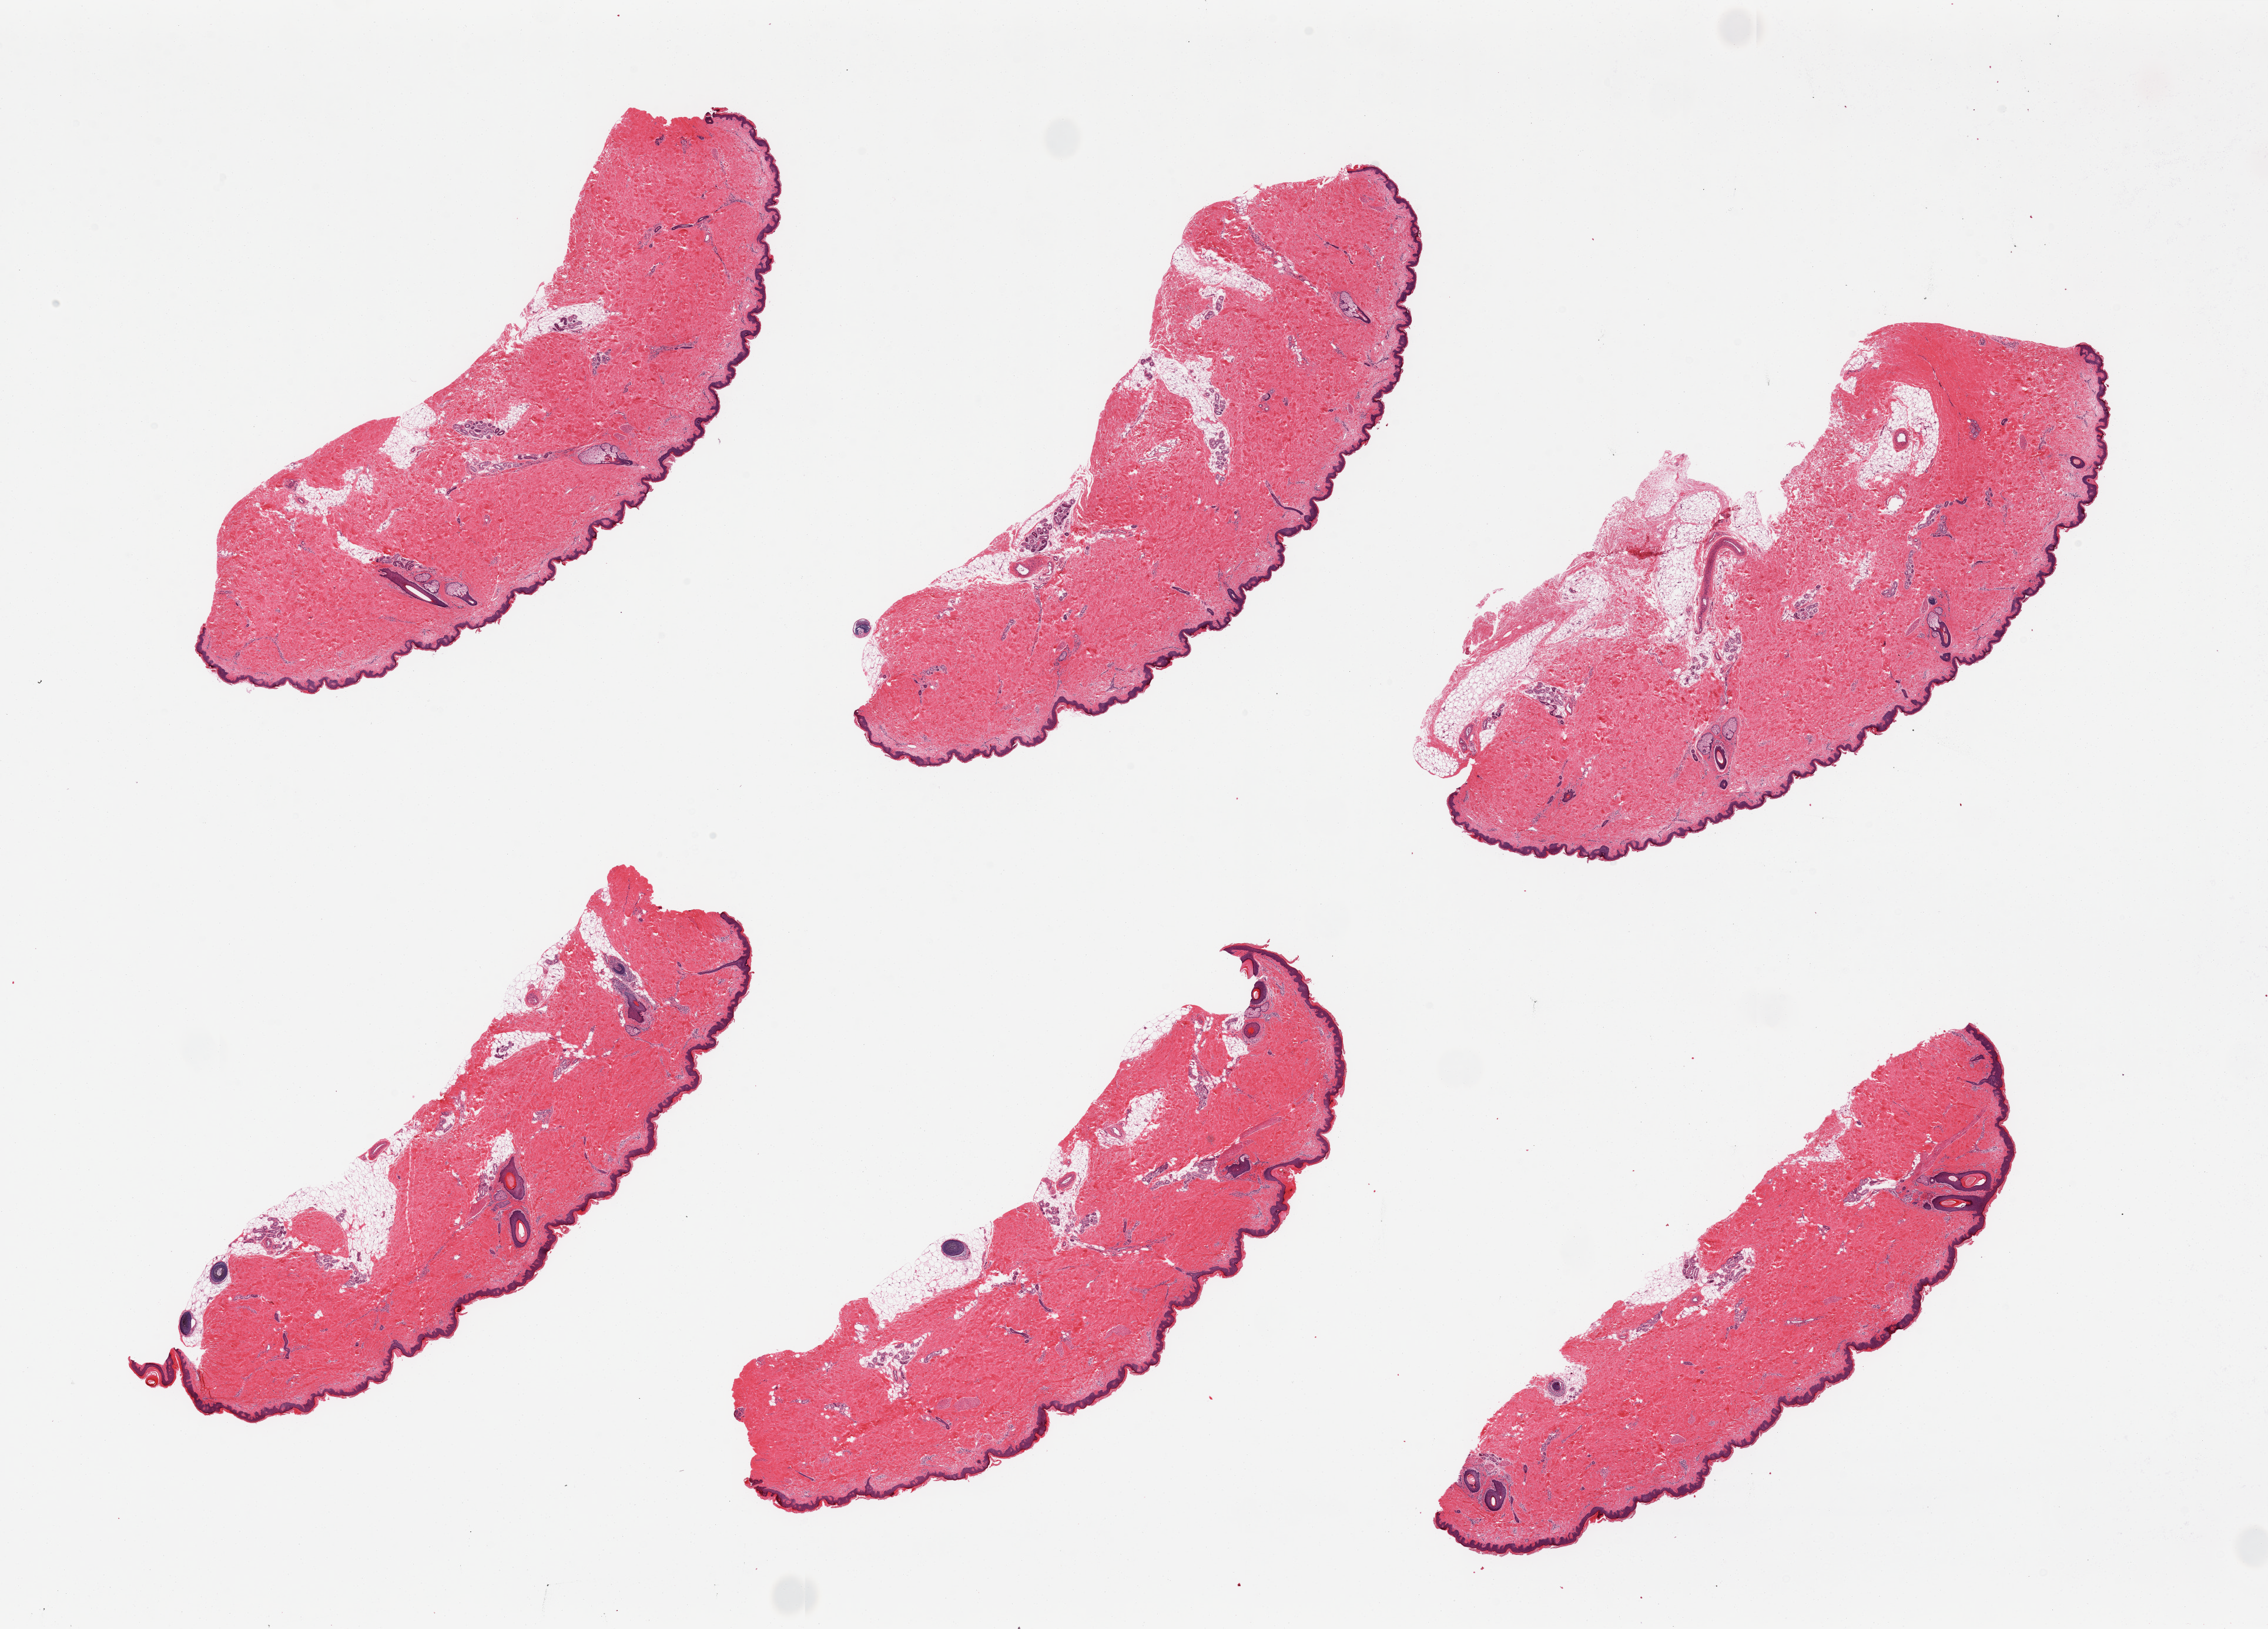
Whole-slide image, H&E stain — low-resolution overview of the scanned area, about 30.5 x 21.9 mm; PAXgene-fixed, paraffin-embedded tissue; section of skin of lower leg (target tissue); donor tissue sample. Donor sex: male.
* pathologist's review note for this sample: 6 pieces, attached and internal adipose tissue up to ~20%, squamous epithelium measured 45 to 54 microns